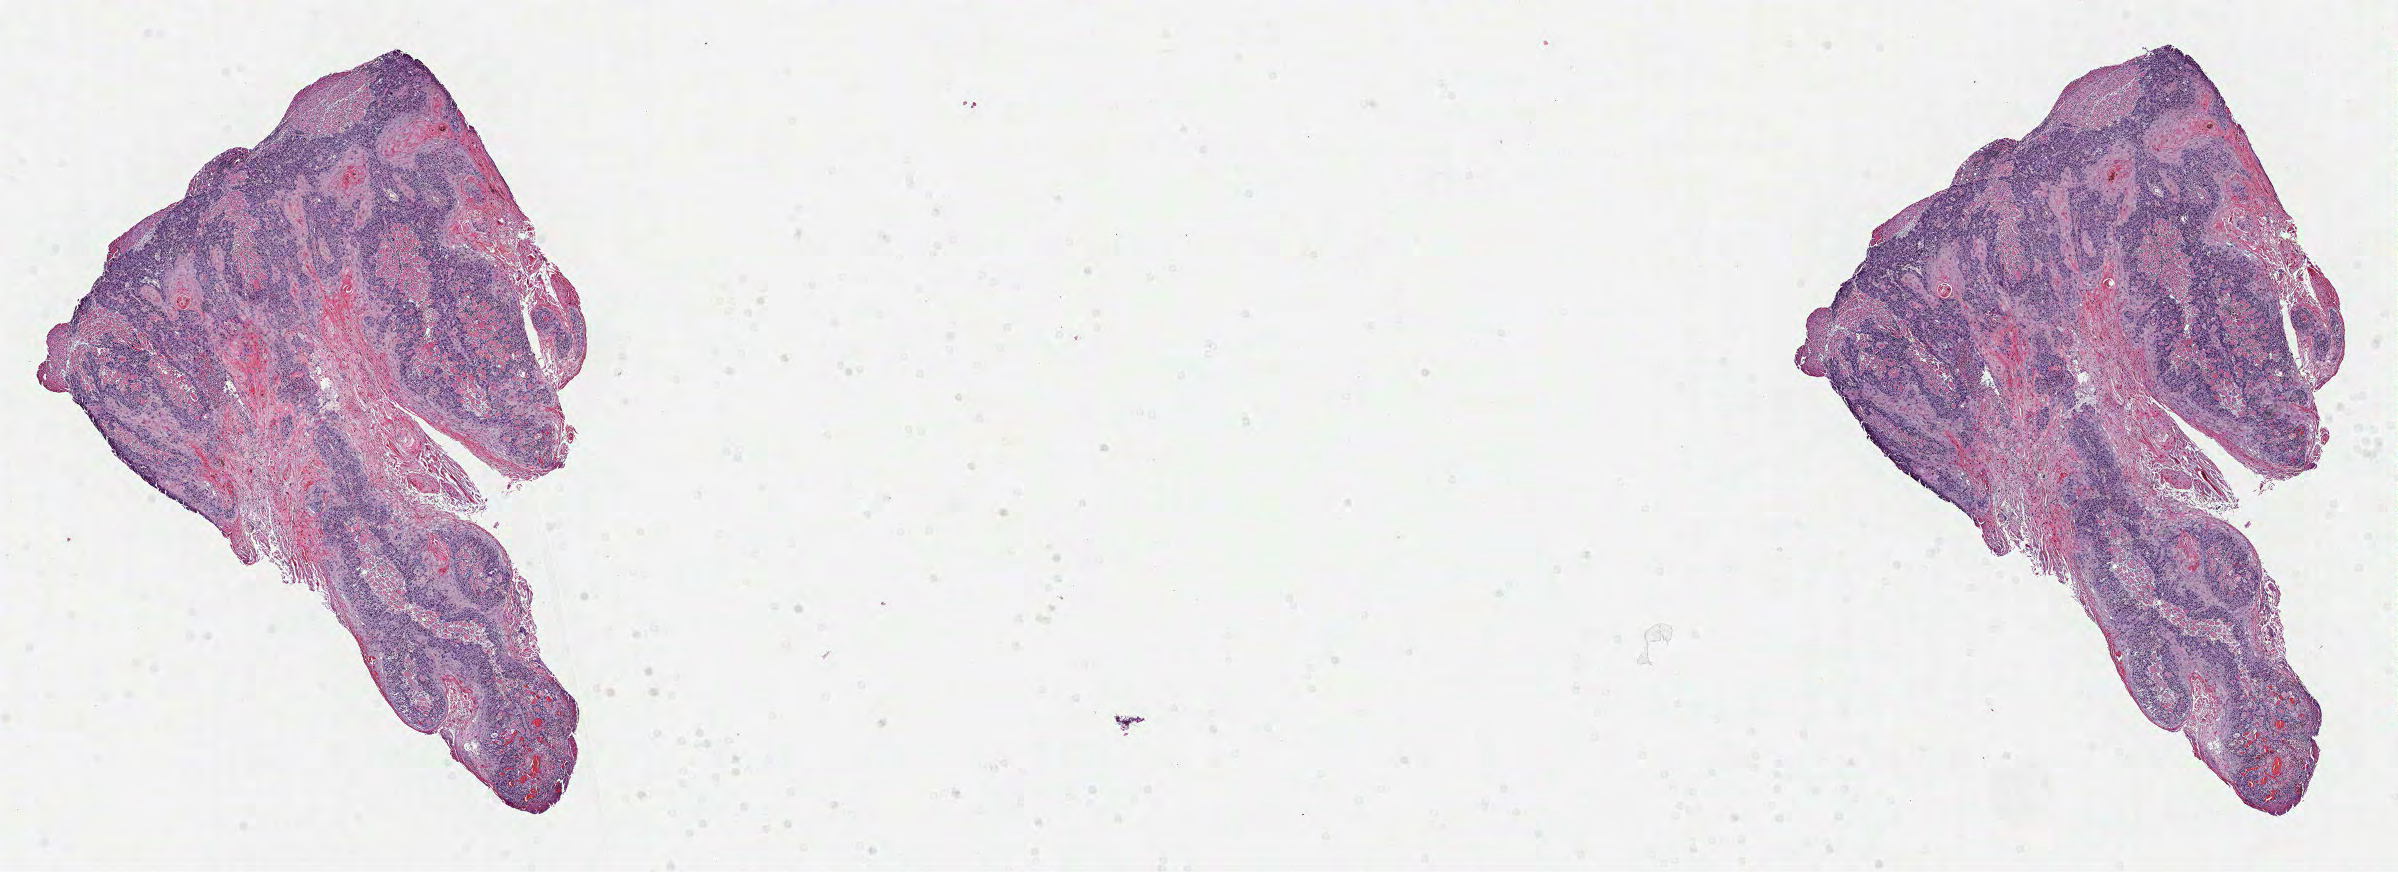
Whole-slide histology image, H&E, a low-resolution overview of the entire scanned area, about 19.3 x 7.0 mm (acquisition: 40x scan); formalin-fixed paraffin-embedded (FFPE) diagnostic section; head and neck, primary tumour sample. Male patient; age at initial diagnosis 60 years.
Diagnosis: Squamous cell carcinoma, NOS (tongue, NOS).